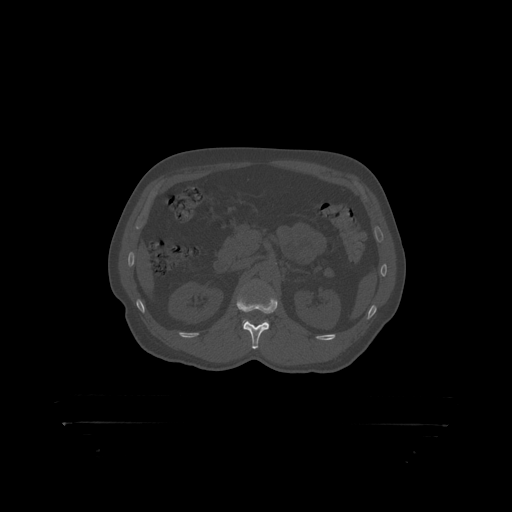
CT including the spine, one axial slice; position 316 of 399 along the scan axis; reconstruction kernel STANDARD; 120 kVp; bone window (W 1800 / L 400 HU); 512 × 512 image matrix, field of view 650 × 650 mm. Male patient, age 46 years. Case-level facts recorded for this patient, not image findings: primary cancer: skin.
Structures marked on this image (semi-automatic segmentation, software-assisted and operator-edited):
- L1 vertebra: bounding box [x1, y1, x2, y2] px = [237, 297, 278, 314]